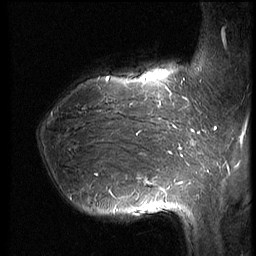
Breast MRI (dynamic contrast-enhanced), one sagittal slice; position 21 of 66 along the scan axis; dynamic contrast-enhanced series, image 2 of 3 at this slice position (ordered by acquisition); 1.5 T; TE 4.2 ms, TR 8.9 ms; 2.5 mm slice thickness; 256 × 256 image matrix. Patient: female, 39 years. From the clinical record (not read from this slice): setting: breast cancer imaged before/during neoadjuvant chemotherapy; receptor status: HER2-positive.
Annotated regions visible in this slice (semi-automatic segmentation, software-assisted and operator-edited):
- analysis volume of interest (the breast-tissue region the enhancement analysis was run in; not a lesion): bounding box <36,75,188,218> (left, top, right, bottom; pixels)
- tumour enhancement mask (voxels above the 140 % enhancement threshold inside the analysis volume of interest): <95,77,182,193>